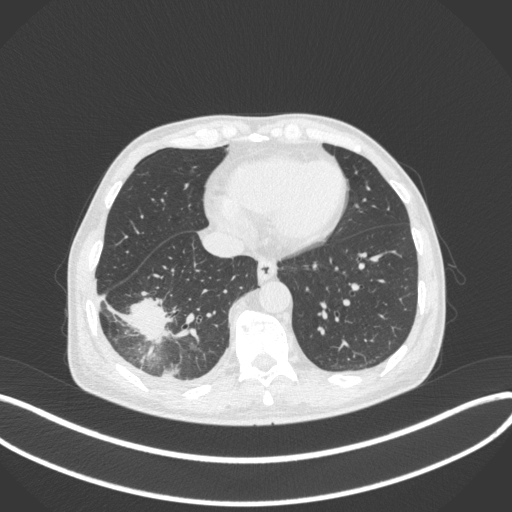
Chest CT, one axial slice. Slice 110 of 385 in the series (ordered by position). Lung window (W 1500 / L -600 HU). 1 mm slice thickness. 512 × 512 image matrix. Male patient, age 64 years. Case-level facts recorded for this patient, not image findings: clinical TNM (as recorded): T3 N0 M0.
Outlined on this slice (bounding box drawn by a radiologist):
- lung tumour (recorded histology: adenocarcinoma): box from (x=119, y=290) to (x=171, y=346) px